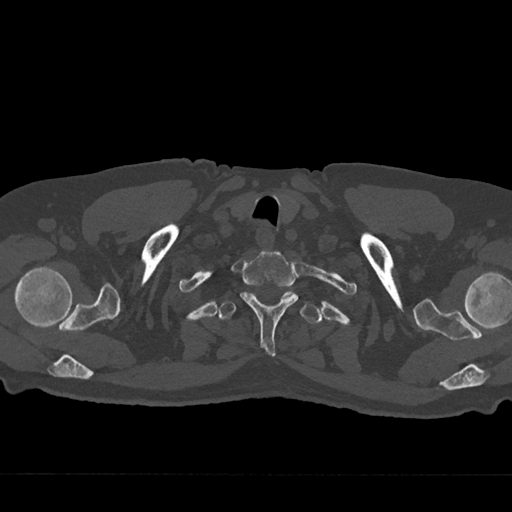
CT including the spine, one axial slice. Slice 648 of 797 in the series (ordered by position). Reconstruction kernel Br40s/3. 120 kVp. Bone window (W 1800 / L 400 HU). 512 × 512 image matrix, field of view 377 × 377 mm. Male patient, age 75 years. Case-level facts recorded for this patient, not image findings: primary cancer: renal.
Annotated regions visible in this slice (semi-automatic segmentation, software-assisted and operator-edited):
- T1 vertebra: bounding box [x1, y1, x2, y2] px = [240, 251, 298, 356]
- T2 vertebra: [218, 290, 322, 324]